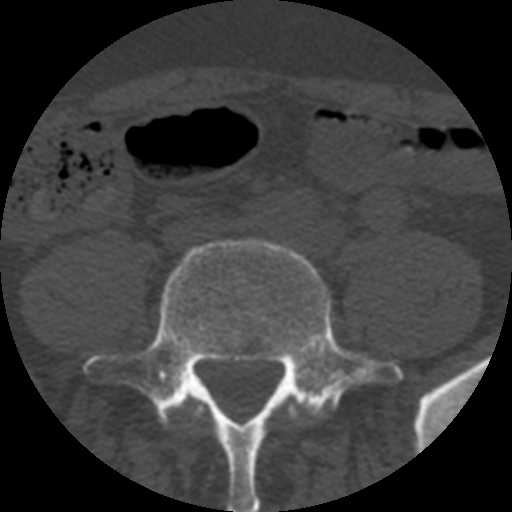
CT including the spine, one axial slice; position 69 of 508 along the scan axis; bone window (W 1800 / L 400 HU); 512 × 512 image matrix, field of view 160 × 160 mm. Patient age 57 years. Case-level facts recorded for this patient, not image findings: primary cancer: prostate.
Structures marked on this image (semi-automatic segmentation, software-assisted and operator-edited):
- L4 vertebra: box from (x=189, y=399) to (x=297, y=419) px
- L5 vertebra: (x=84, y=240)–(x=403, y=512)